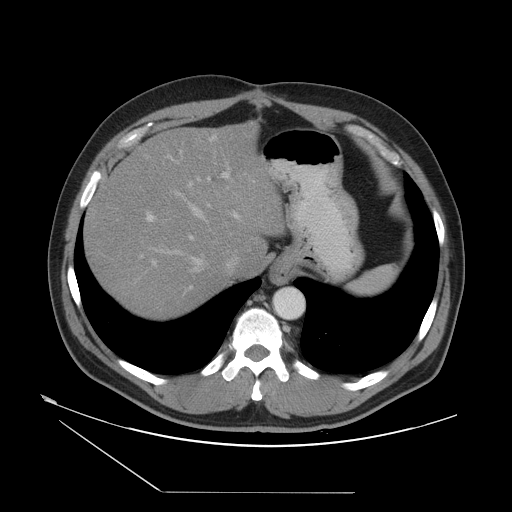
Contrast-enhanced abdominal CT, one axial slice; slice 40 of 55 in the series (ordered by position); reconstruction kernel STANDARD; soft-tissue window (W 400 / L 40 HU); 5 mm slice thickness; 512 × 512 image matrix, field of view 454 × 454 mm. Male patient, age 59 years. From the clinical record (not read from this slice): diagnosis: colorectal cancer liver metastases, imaged before liver resection; multiple liver metastases: yes.
Structures marked on this image (outlined manually by an expert reader):
- hepatic veins: bounding box <150,174,254,293> (left, top, right, bottom; pixels)
- liver: <88,128,281,315>
- planned liver remnant (the part of the liver to remain after resection): <88,151,266,316>
- portal vein (with intrahepatic branches): <139,155,230,289>
- liver metastasis: <97,262,105,270>